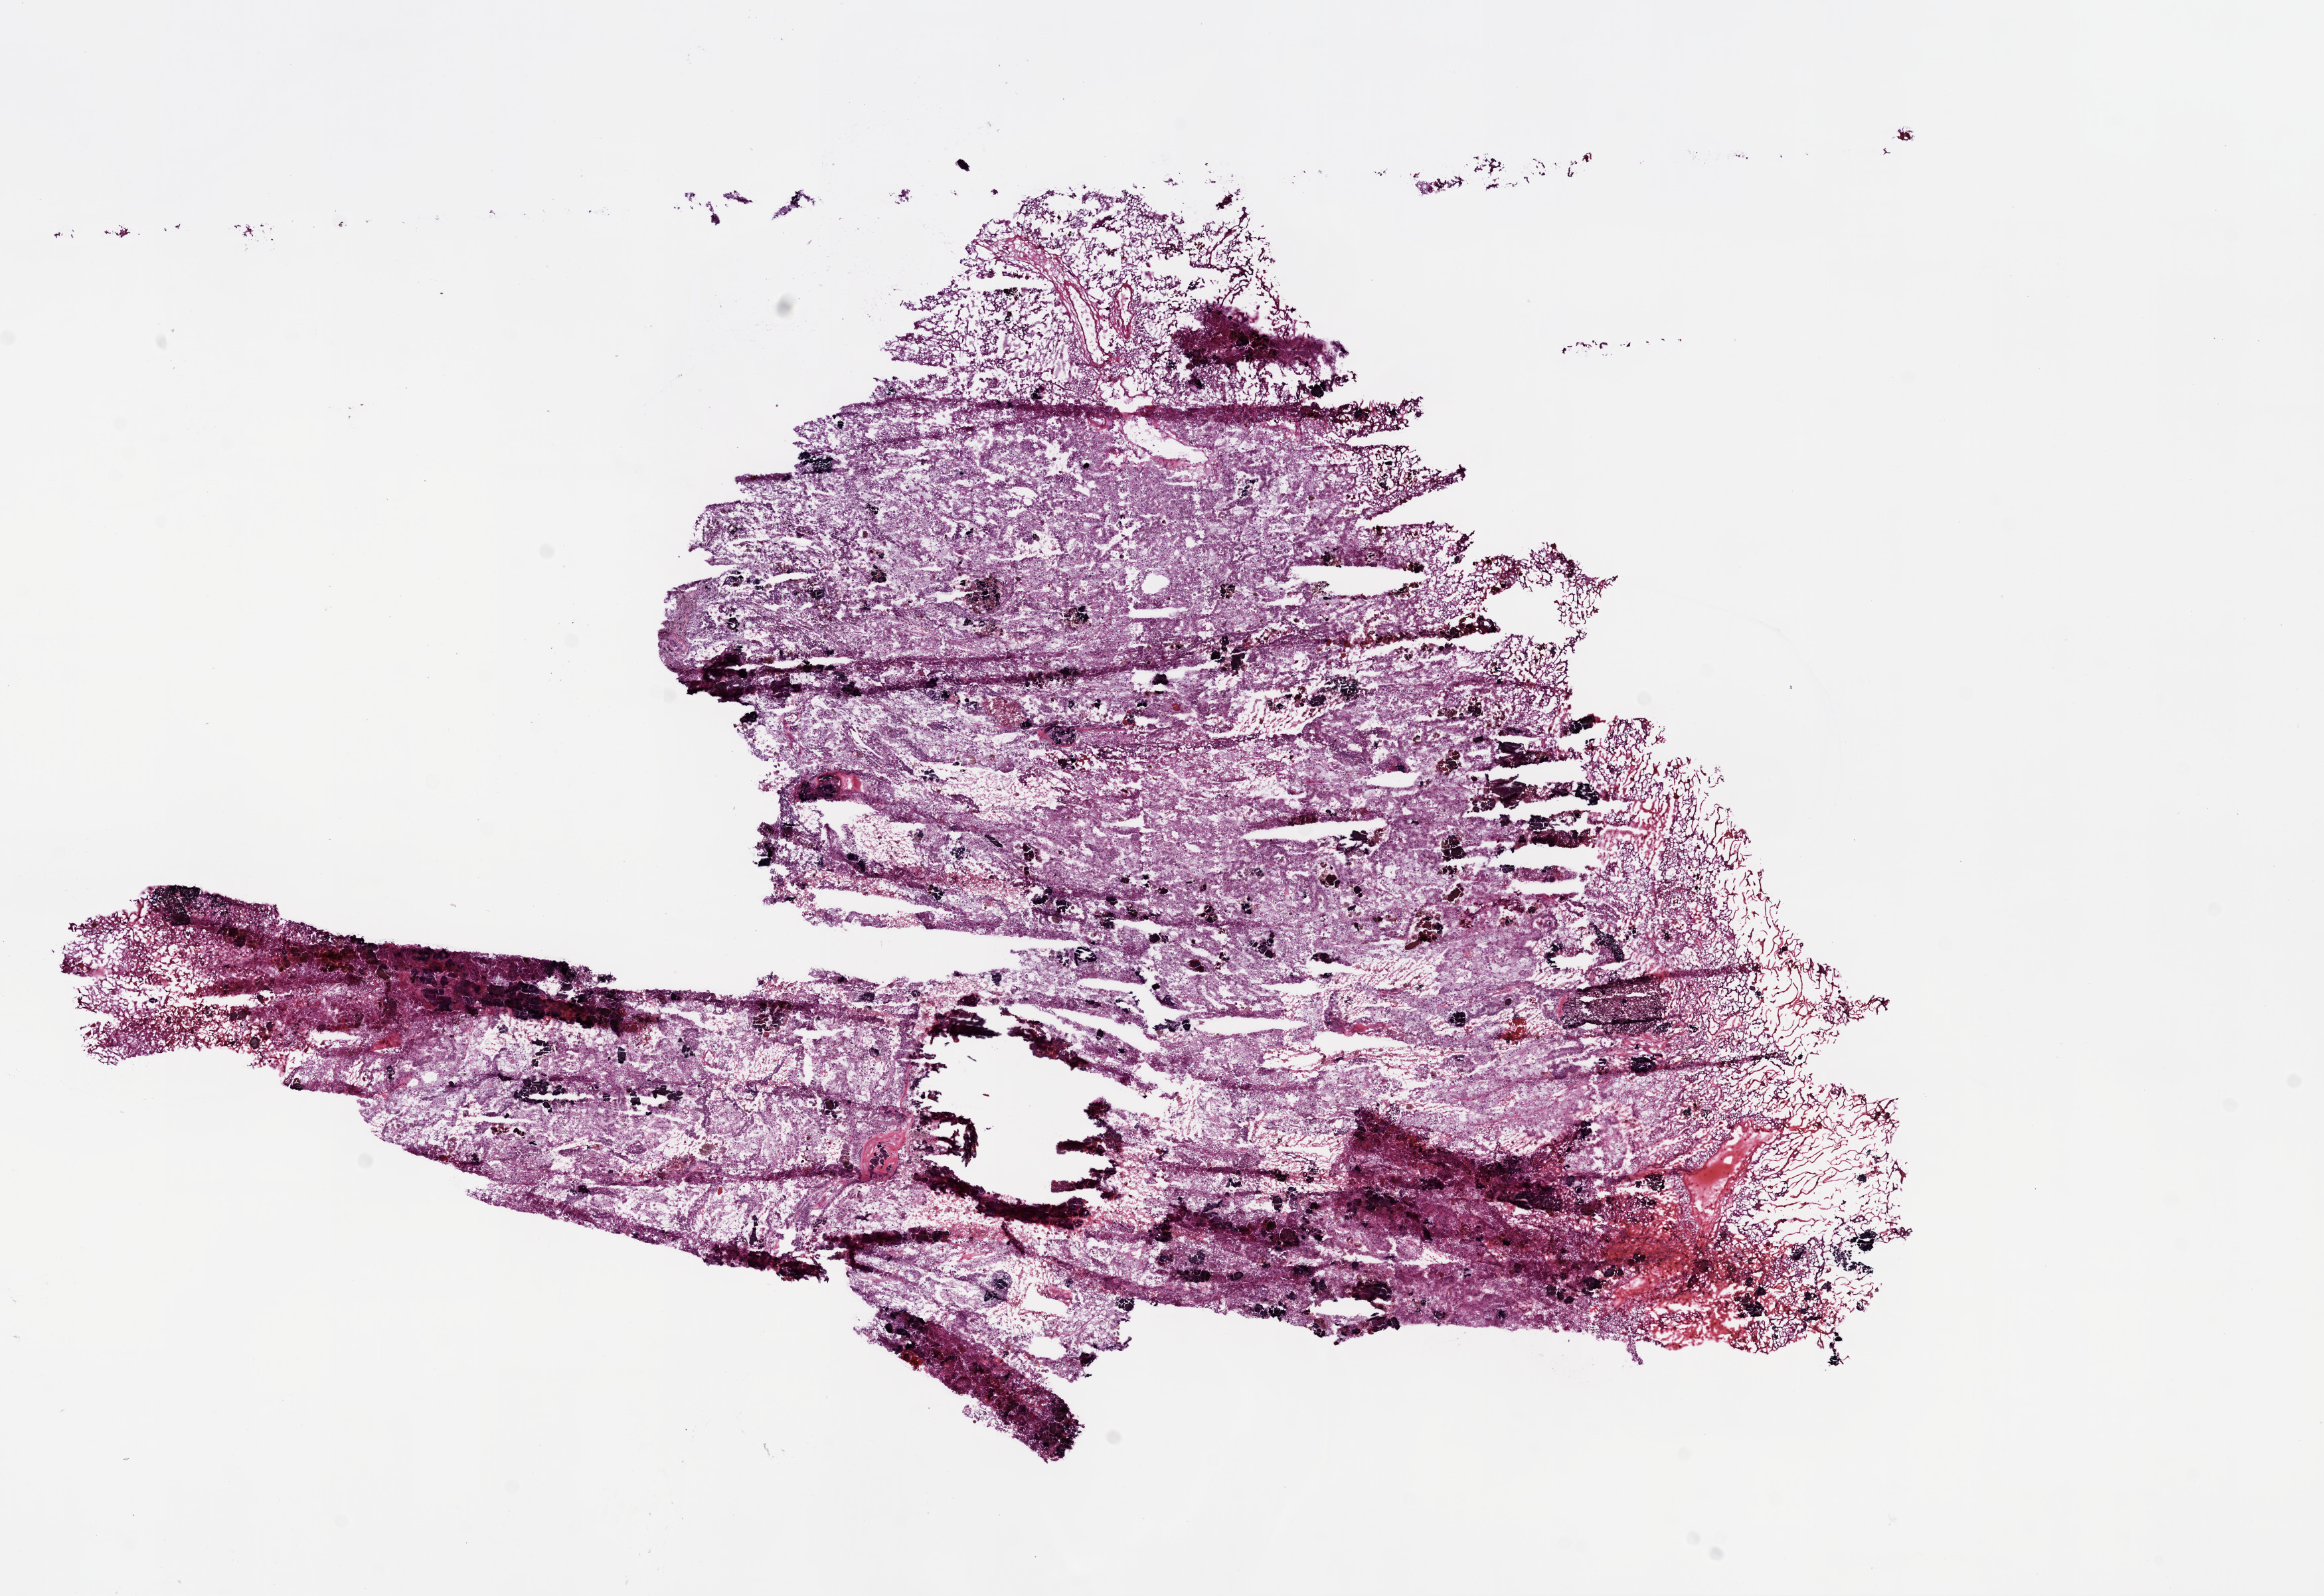
H&E whole-slide image — a low-resolution overview of the entire scanned area, about 14.0 x 9.6 mm (from a 20x scan); frozen section from the bottom of the tissue portion; sample: primary tumour, kidney. Female, age 51 years at initial diagnosis. Histologic grade: G2 (moderately differentiated). Slide review estimates, as recorded: tumour cells 90%, tumour nuclei 85%, normal cells 0%, stromal cells 10%, necrosis 0%.
Diagnosis: Clear cell adenocarcinoma, NOS. AJCC pathologic stage: I.